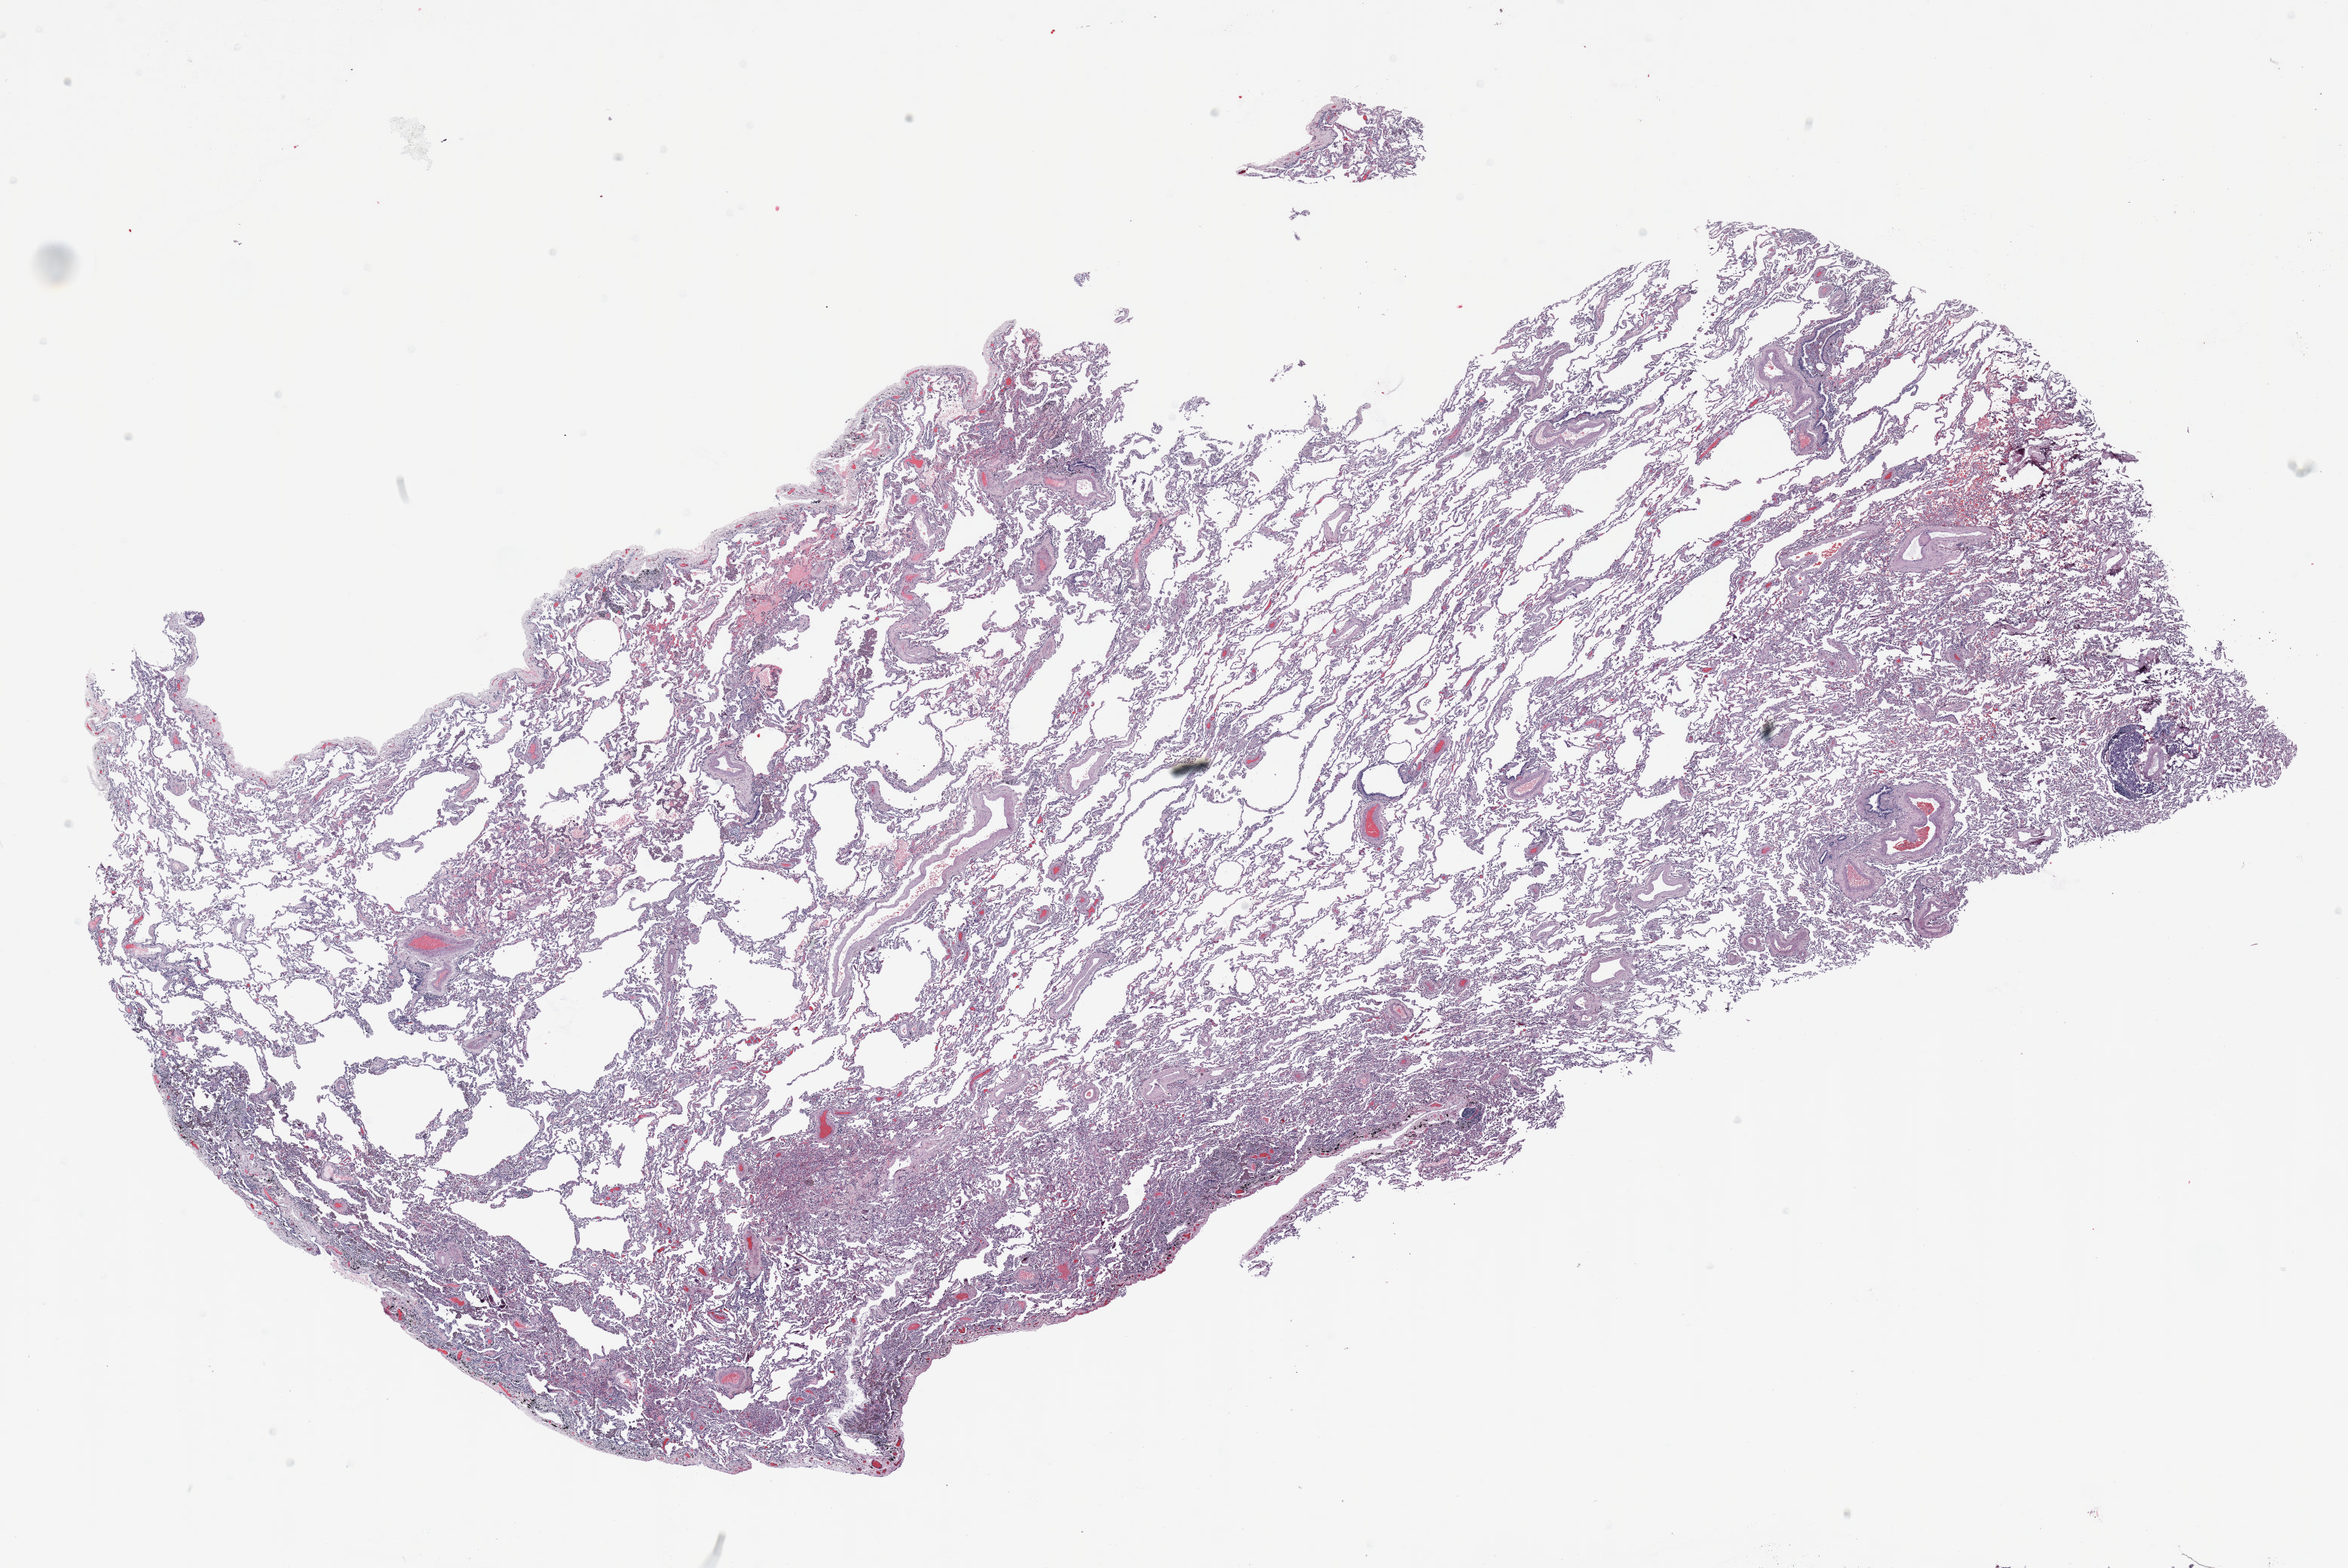
Whole-slide histology image, H&E-stained, whole scanned area (about 25.0 x 16.7 mm) shown as a low-resolution overview, FFPE section, lung tissue. Male patient, aged 65 at enrolment. Grade: moderately differentiated (G2).
Stage (AJCC 6th edition): IA. Tumour size (pathology): 15 mm. Participant's lung-cancer diagnosis: Adenocarcinoma, NOS. Primary tumour location (clinical record): right middle lobe.